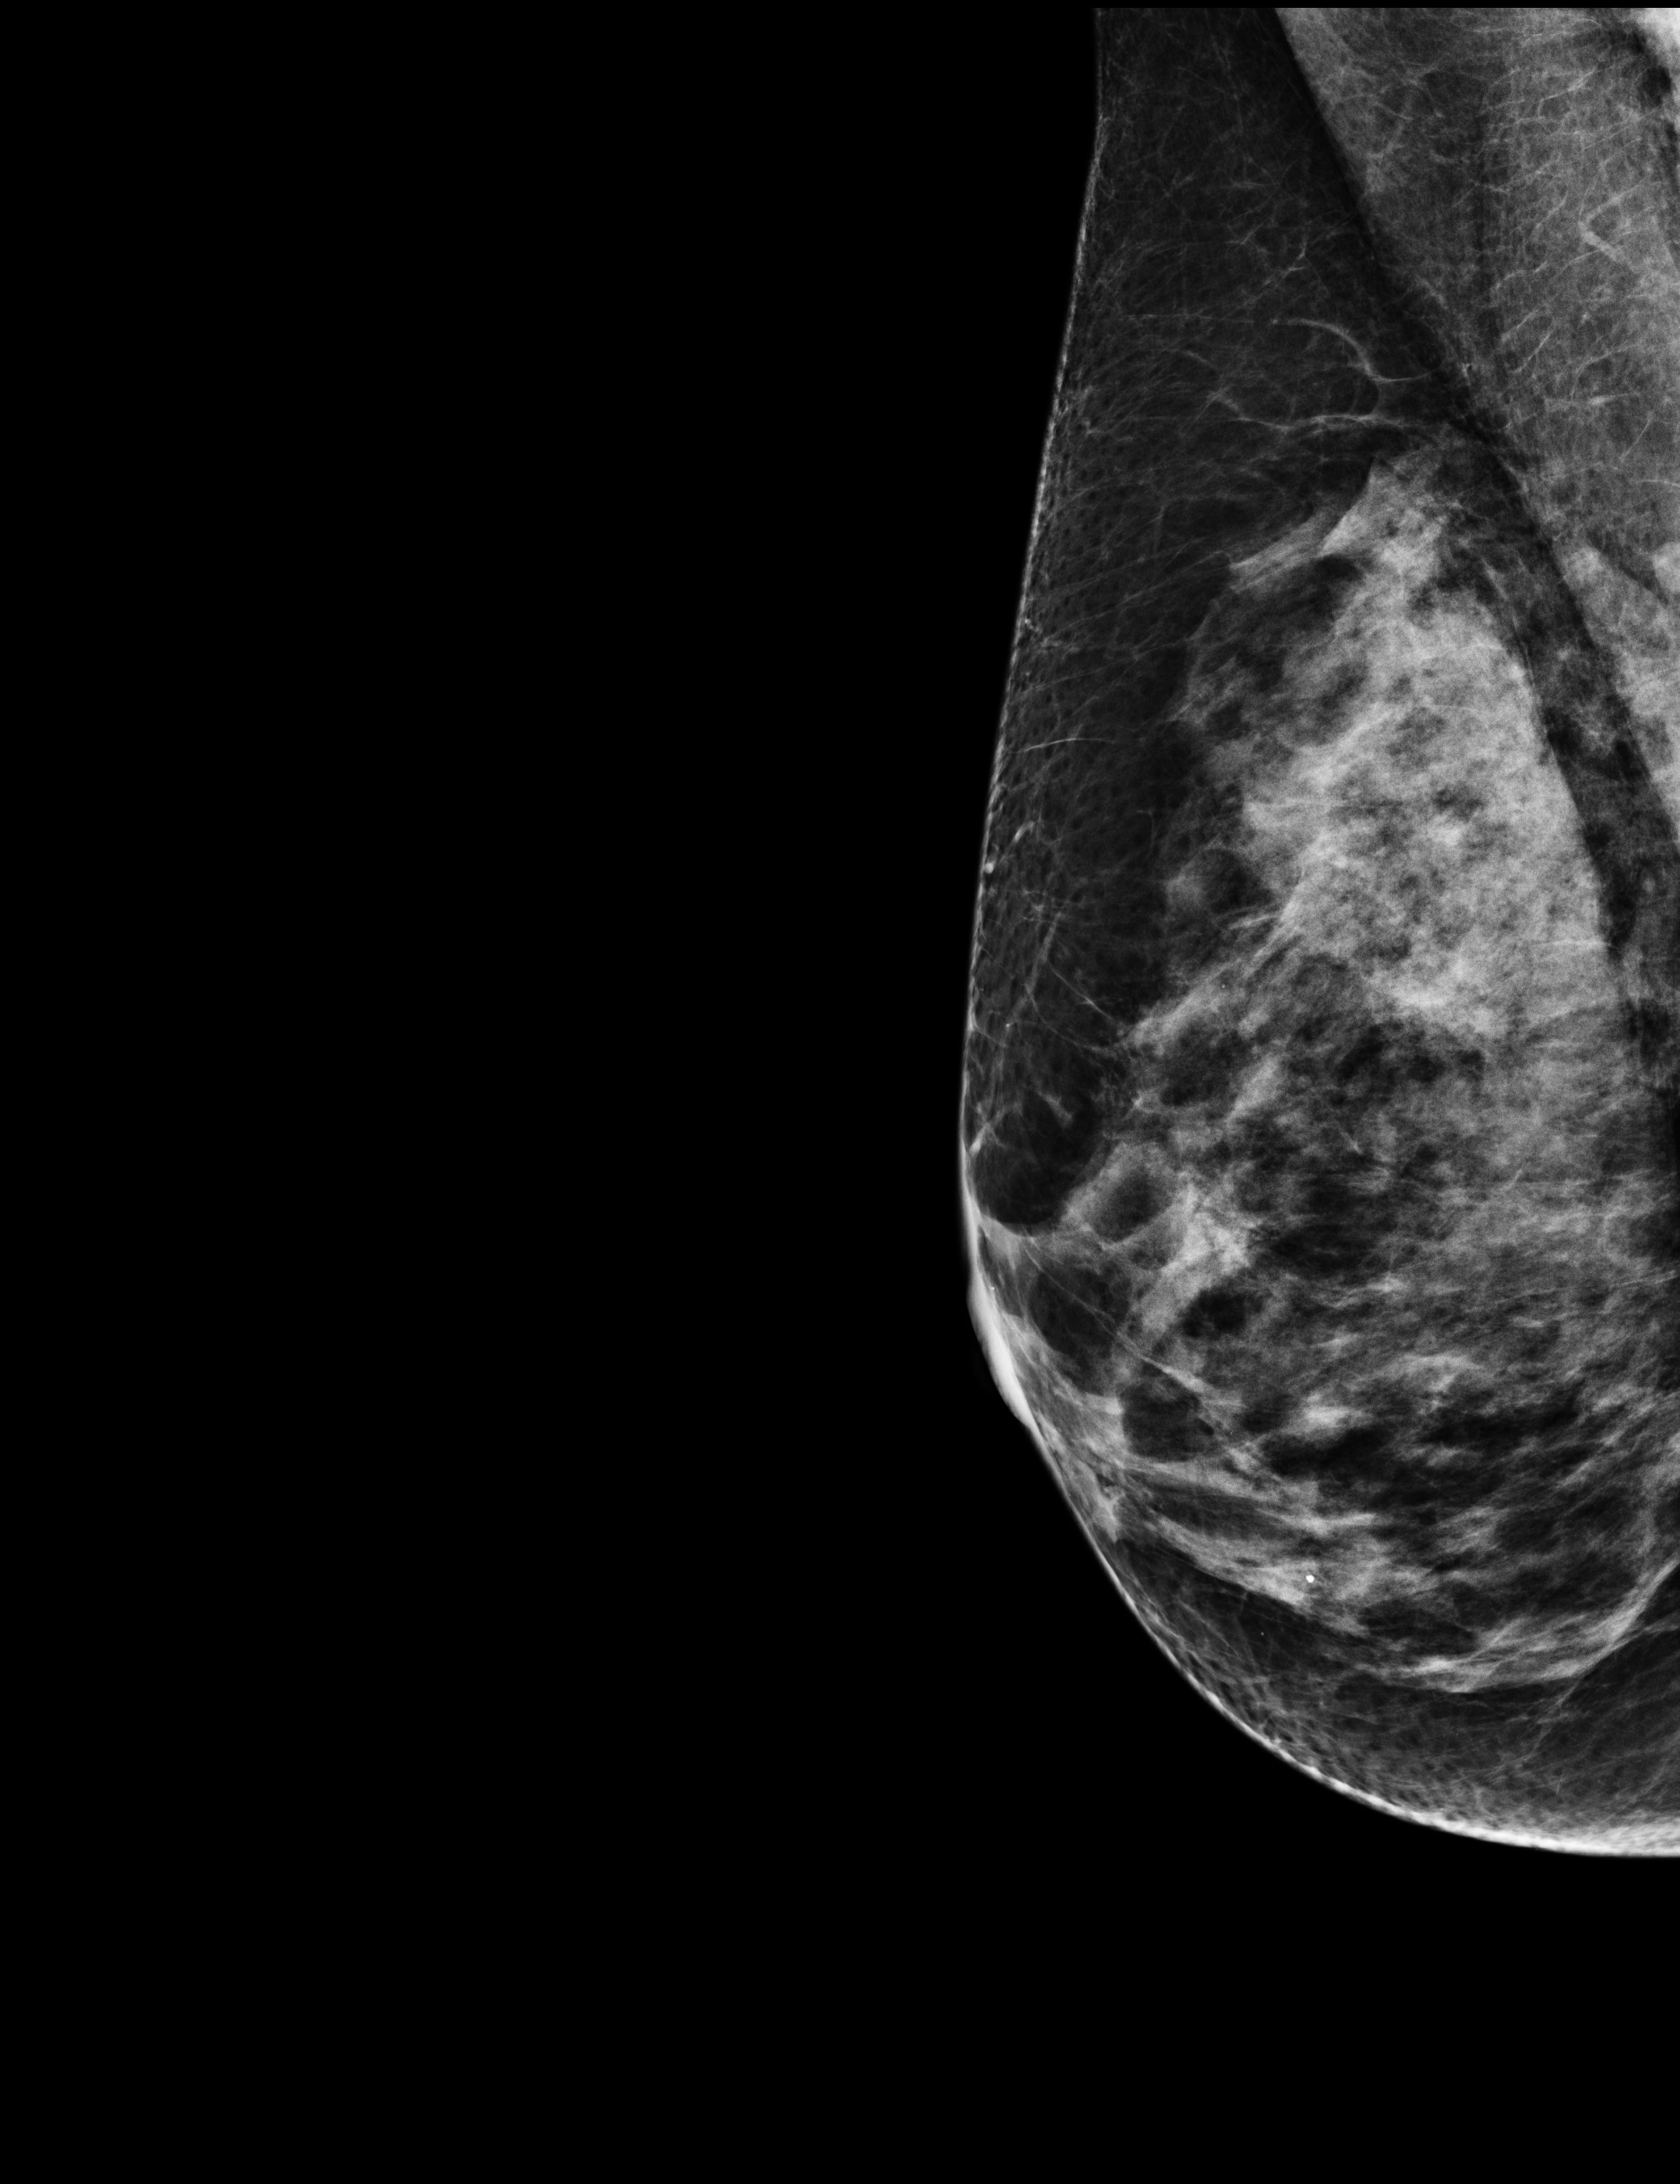
Full-field digital mammogram (FFDM), right breast, mediolateral oblique (MLO) view, annual screening mammography examination, compressed breast thickness 59 mm. Female patient, age 64 years.
Breast density at the screening exam (both breasts): extremely dense (BI-RADS density category d). Final BI-RADS category for the screening round (tomosynthesis exam, both breasts): category 1. Recall: no recall after this screen.